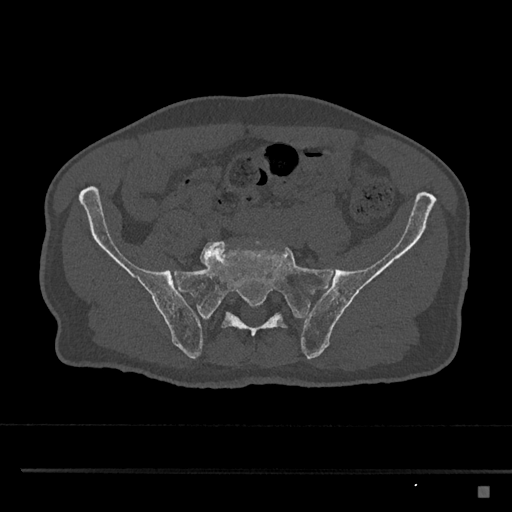
CT including the spine, one axial slice. Position 526 of 797 along the scan axis. Reconstruction kernel Br40s/3. 120 kVp. Bone window (W 1800 / L 400 HU). 512 × 512 image matrix, field of view 391 × 391 mm. Patient: male, 59 years. Case-level facts recorded for this patient, not image findings: primary cancer: prostate.
Structures marked on this image (semi-automatic segmentation, software-assisted and operator-edited):
- L5 vertebra: bounding box <200,239,269,267> (left, top, right, bottom; pixels)